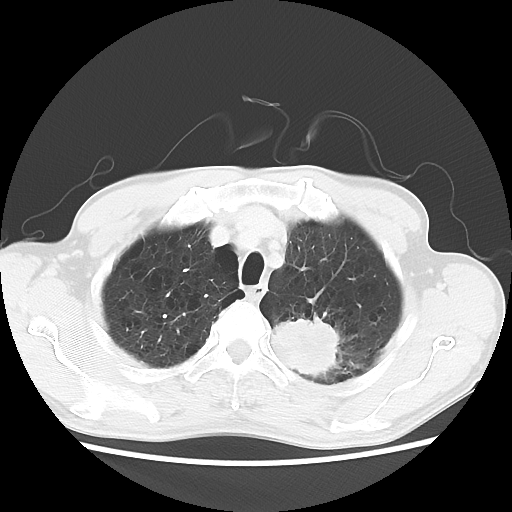
Chest CT, one axial slice. Slice 53 of 64 in the series (ordered by position). Reconstruction kernel LUNG. 120 kVp. Lung window (W 1500 / L -600 HU). 512 × 512 image matrix, field of view 346 × 346 mm. Patient: male, 63 years. Case-level facts recorded for this patient, not image findings: clinical TNM (as recorded): T2 N0 M0.
Structures marked on this image (bounding box drawn by a radiologist):
- lung tumour (recorded histology: adenocarcinoma): box from (x=267, y=309) to (x=353, y=379) px